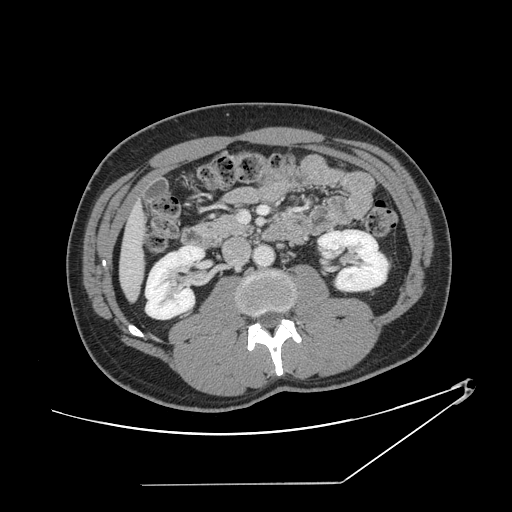
Contrast-enhanced abdominal CT, one axial slice; position 49 of 152 along the scan axis; reconstruction kernel STANDARD; intravenous contrast given; soft-tissue window (W 400 / L 40 HU); 512 × 512 image matrix. Male patient, age 45 years. From the clinical record (not read from this slice): diagnosis: colorectal cancer liver metastases, imaged before liver resection; multiple liver metastases: no; largest metastasis: 1 cm.
Outlined on this slice (expert manual segmentation):
- hepatic veins: bounding box [x1, y1, x2, y2] px = [135, 241, 137, 243]
- liver: [121, 209, 144, 298]
- planned liver remnant (the part of the liver to remain after resection): [121, 210, 144, 298]
- portal vein (with intrahepatic branches): [240, 206, 268, 221]